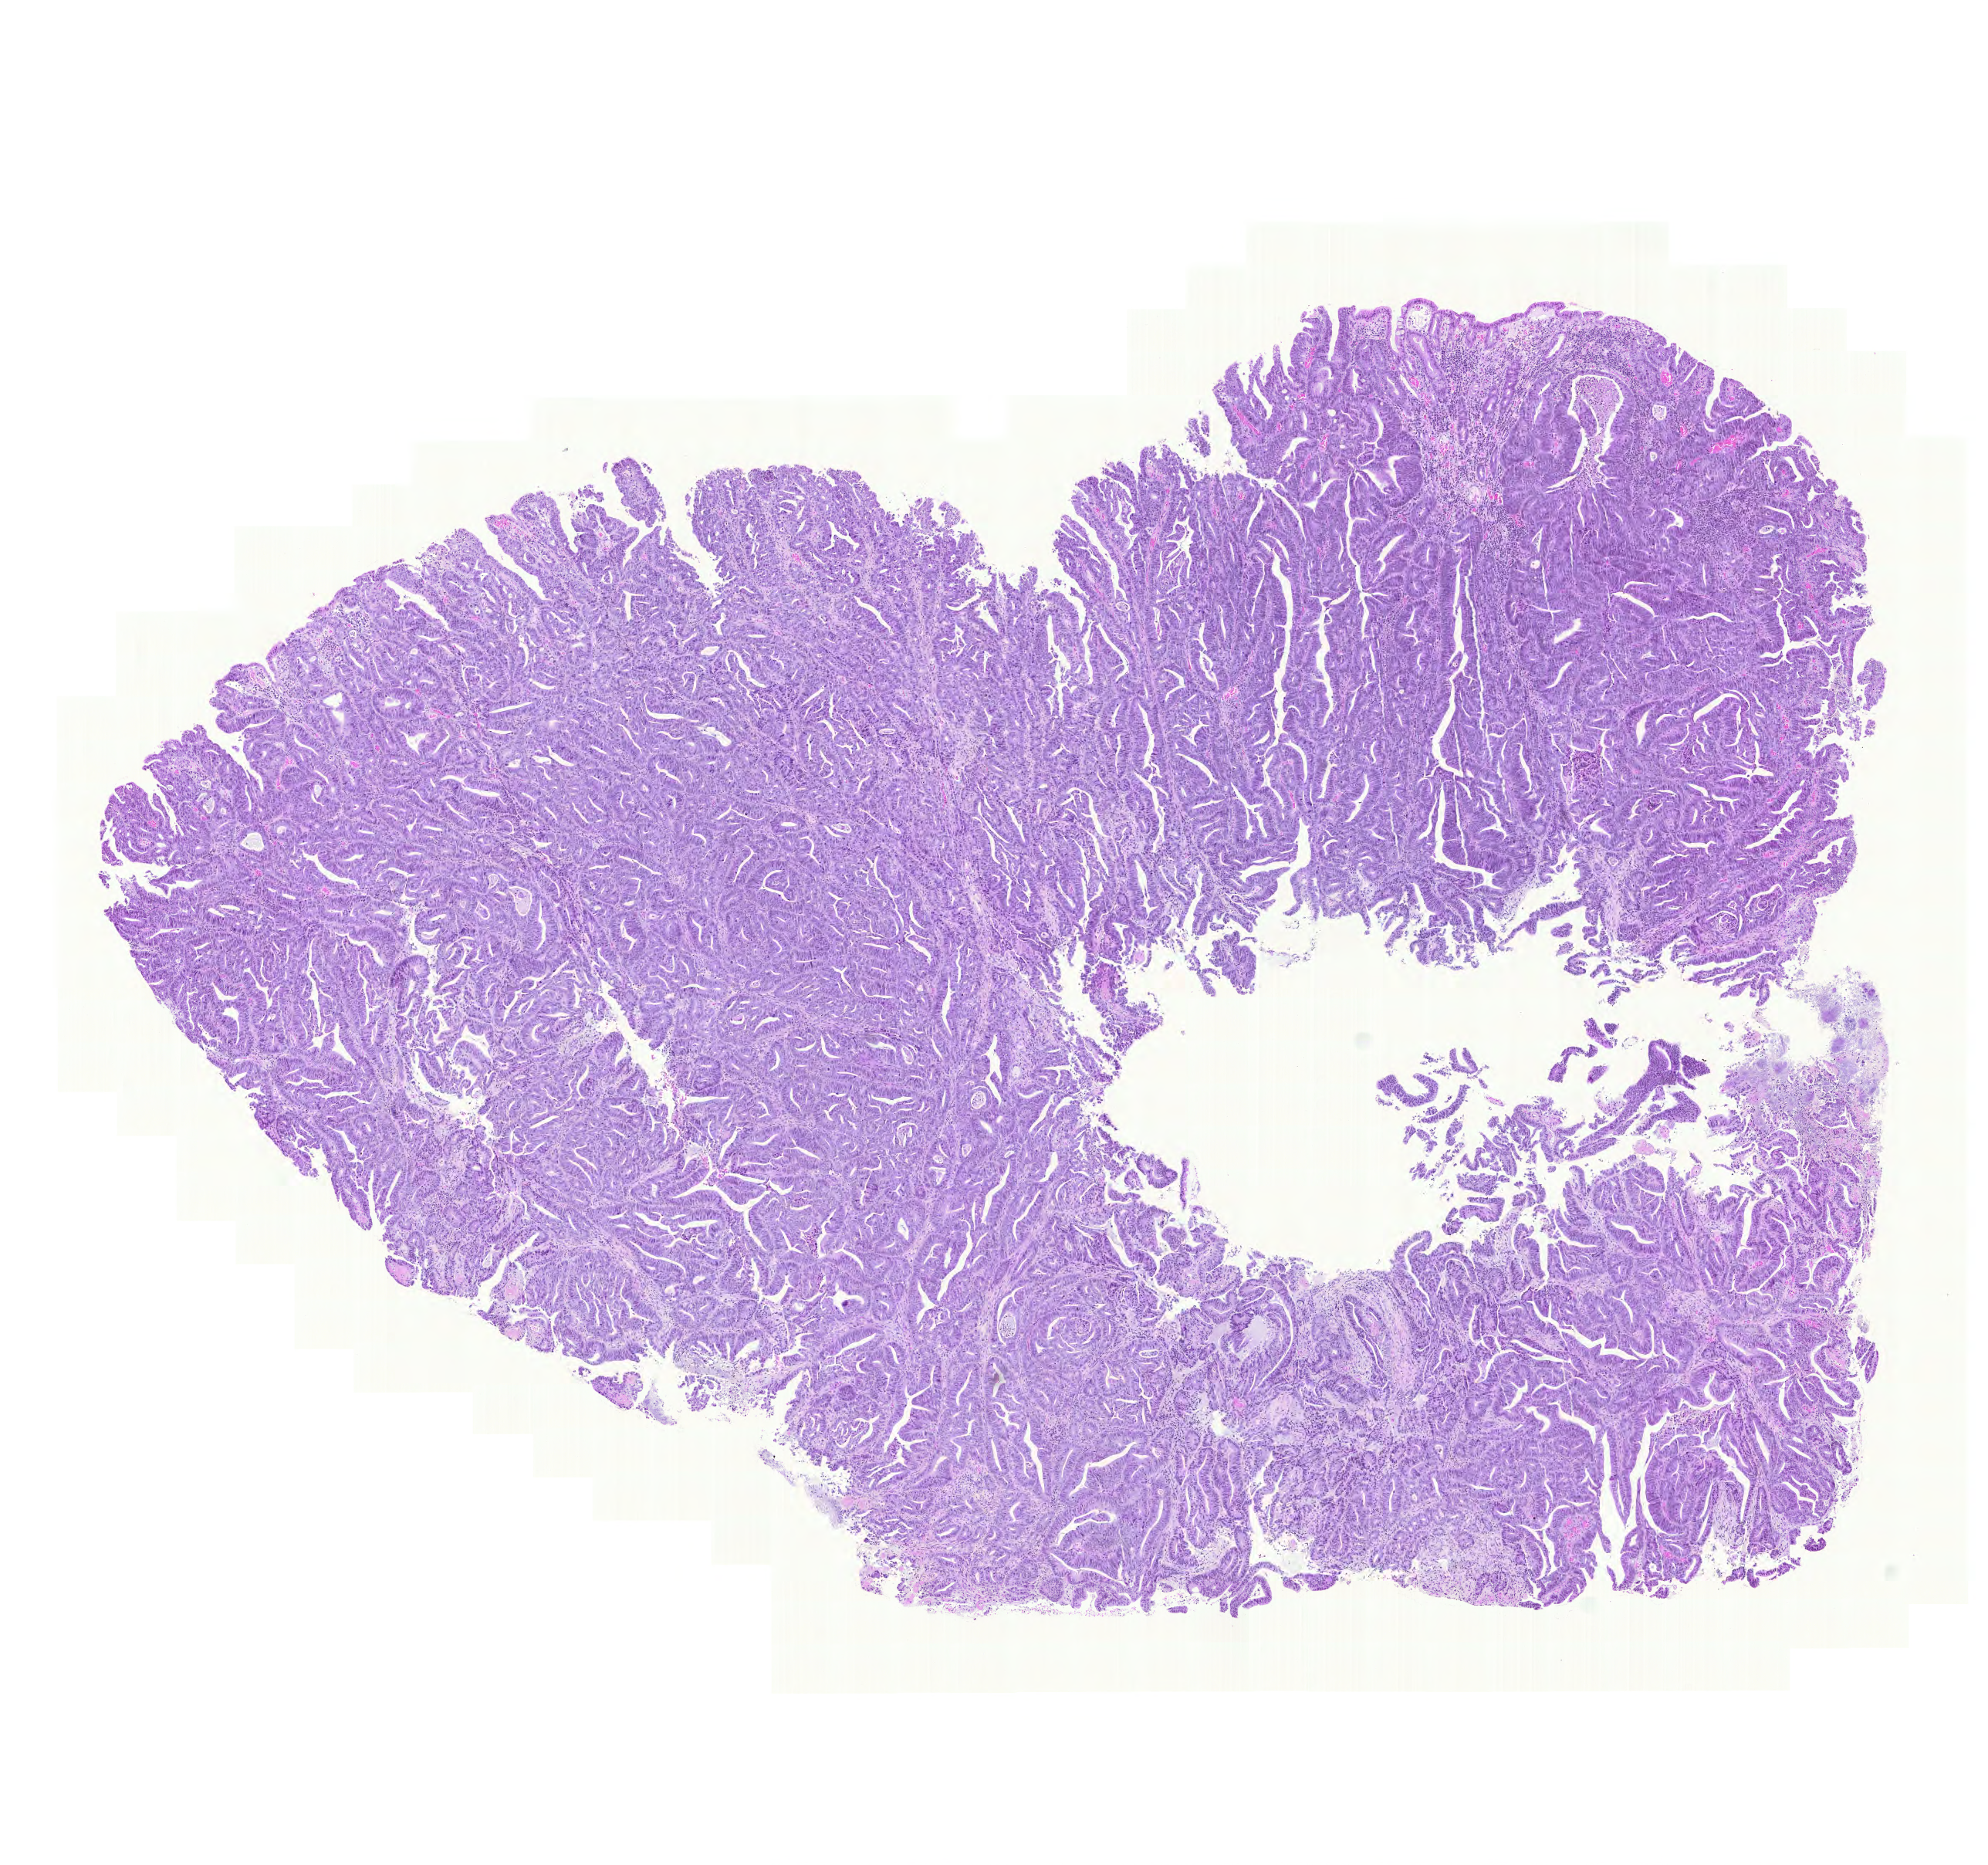
Whole-slide histology image, Hematoxylin and eosin (H&E) stained — shown as a low-resolution overview of the whole scanned area (about 9.6 x 9.0 mm), formalin-fixed paraffin-embedded (FFPE) diagnostic section, primary tumour sample from the colon. Patient: female, age at initial diagnosis 77 years.
Histologic diagnosis: Adenocarcinoma, NOS.